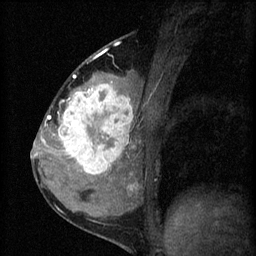
Breast MRI (dynamic contrast-enhanced), one sagittal slice. Position 28 of 60 along the scan axis. 3 images stored at this slice position (order not interpretable as contrast timing). 1.5 T. TE 4.2 ms, TR 8.2 ms. 2 mm slice thickness. 256 × 256 image matrix, field of view 180 × 180 mm. Female patient, age 37 years.
Annotated regions visible in this slice (semi-automatic segmentation, software-assisted and operator-edited):
- analysis volume of interest (the breast-tissue region the enhancement analysis was run in; not a lesion): box from (x=53, y=78) to (x=140, y=181) px
- tumour enhancement mask (voxels above the 70 % enhancement threshold inside the analysis volume of interest): (x=57, y=78)–(x=133, y=175)